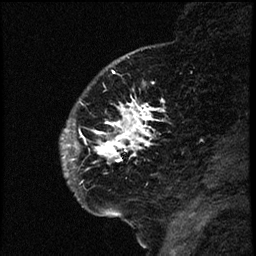
Breast MRI (dynamic contrast-enhanced), one sagittal slice. Slice 16 of 66 in the series (ordered by position). Dynamic contrast-enhanced study with each time point stored as its own series, time point 2 of 3 at this slice position (early post-contrast, ordered by acquisition time). 1.5 T. TE 4.2 ms, TR 17.6 ms. 2 mm slice thickness. 256 × 256 image matrix, field of view 200 × 200 mm. Female patient. From the clinical record (not read from this slice): setting: breast cancer imaged before/during neoadjuvant chemotherapy; receptor status: HER2-positive.
Outlined on this slice (semi-automatic segmentation, software-assisted and operator-edited):
- analysis volume of interest (the breast-tissue region the enhancement analysis was run in; not a lesion): bounding box (x1, y1, x2, y2) in pixels: (63, 69, 177, 209)
- tumour enhancement mask (voxels above the 100 % enhancement threshold inside the analysis volume of interest): (64, 100, 164, 163)